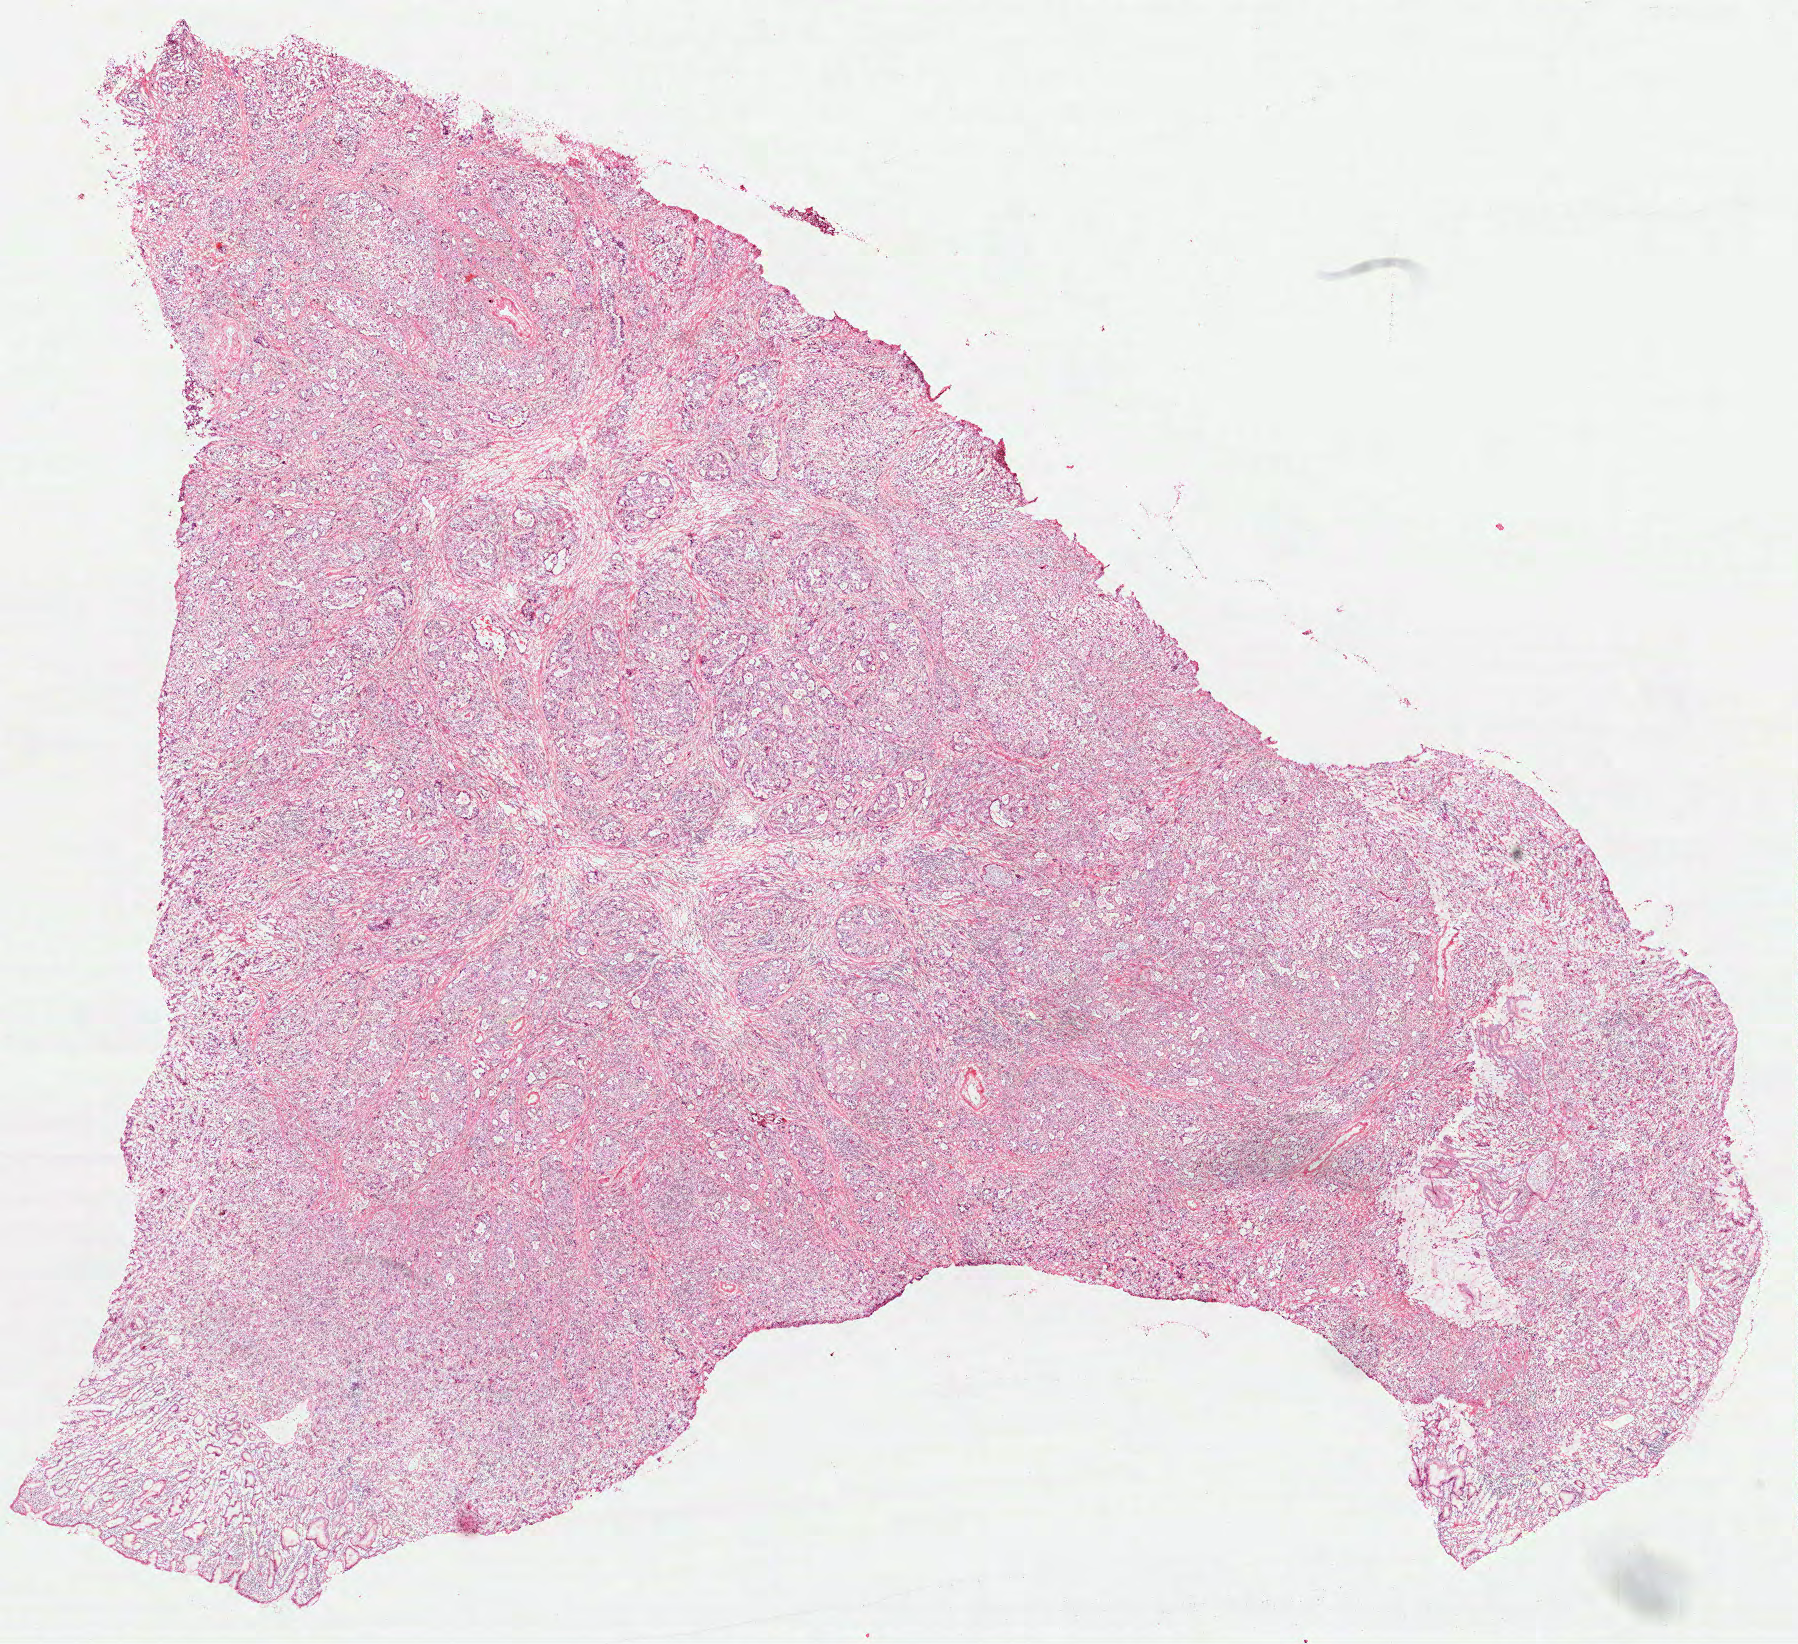
Hematoxylin and eosin (H&E) stained whole-slide image, low-resolution overview of the scanned area, about 14.5 x 13.3 mm (acquisition: 40x scan); frozen section from the top of the tissue portion; primary tumour sample from the stomach. Male patient; age at initial diagnosis 61 years. Histologic grade: G2 (moderately differentiated). Composition of this section per pathologist review: tumour cells 85%, tumour nuclei 70%, normal cells 15%, stromal cells 0%, necrosis 0%. Infiltration values recorded for this section: lymphocyte infiltration 20%, monocyte infiltration 0%, neutrophil infiltration 5%.
* AJCC pathologic stage: IIIA
* lymph nodes positive (case pathology): 2 of 7 examined
* histologic diagnosis: Adenocarcinoma, NOS (fundus of stomach)